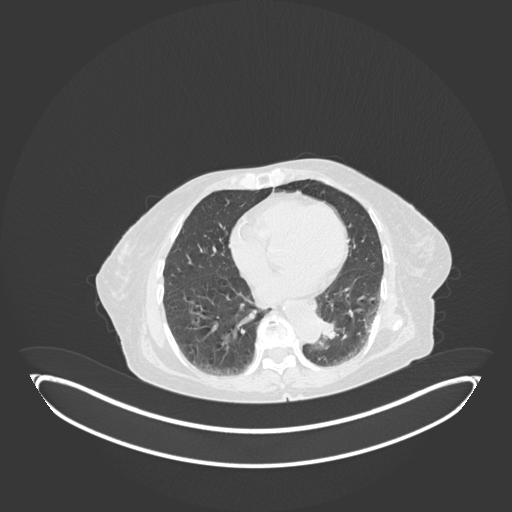
Chest CT, one axial slice. Position 32 of 189 along the scan axis. Lung window (W 1500 / L -600 HU). 1 mm slice thickness. 512 × 512 image matrix, field of view 500 × 500 mm. Female patient, age 82 years. Case-level facts recorded for this patient, not image findings: clinical TNM (as recorded): T1b N0 M1.
Structures marked on this image (rectangle marked by the reading radiologist):
- lung tumour (recorded histology: adenocarcinoma): bounding box (x1, y1, x2, y2) in pixels: (319, 317, 342, 347)